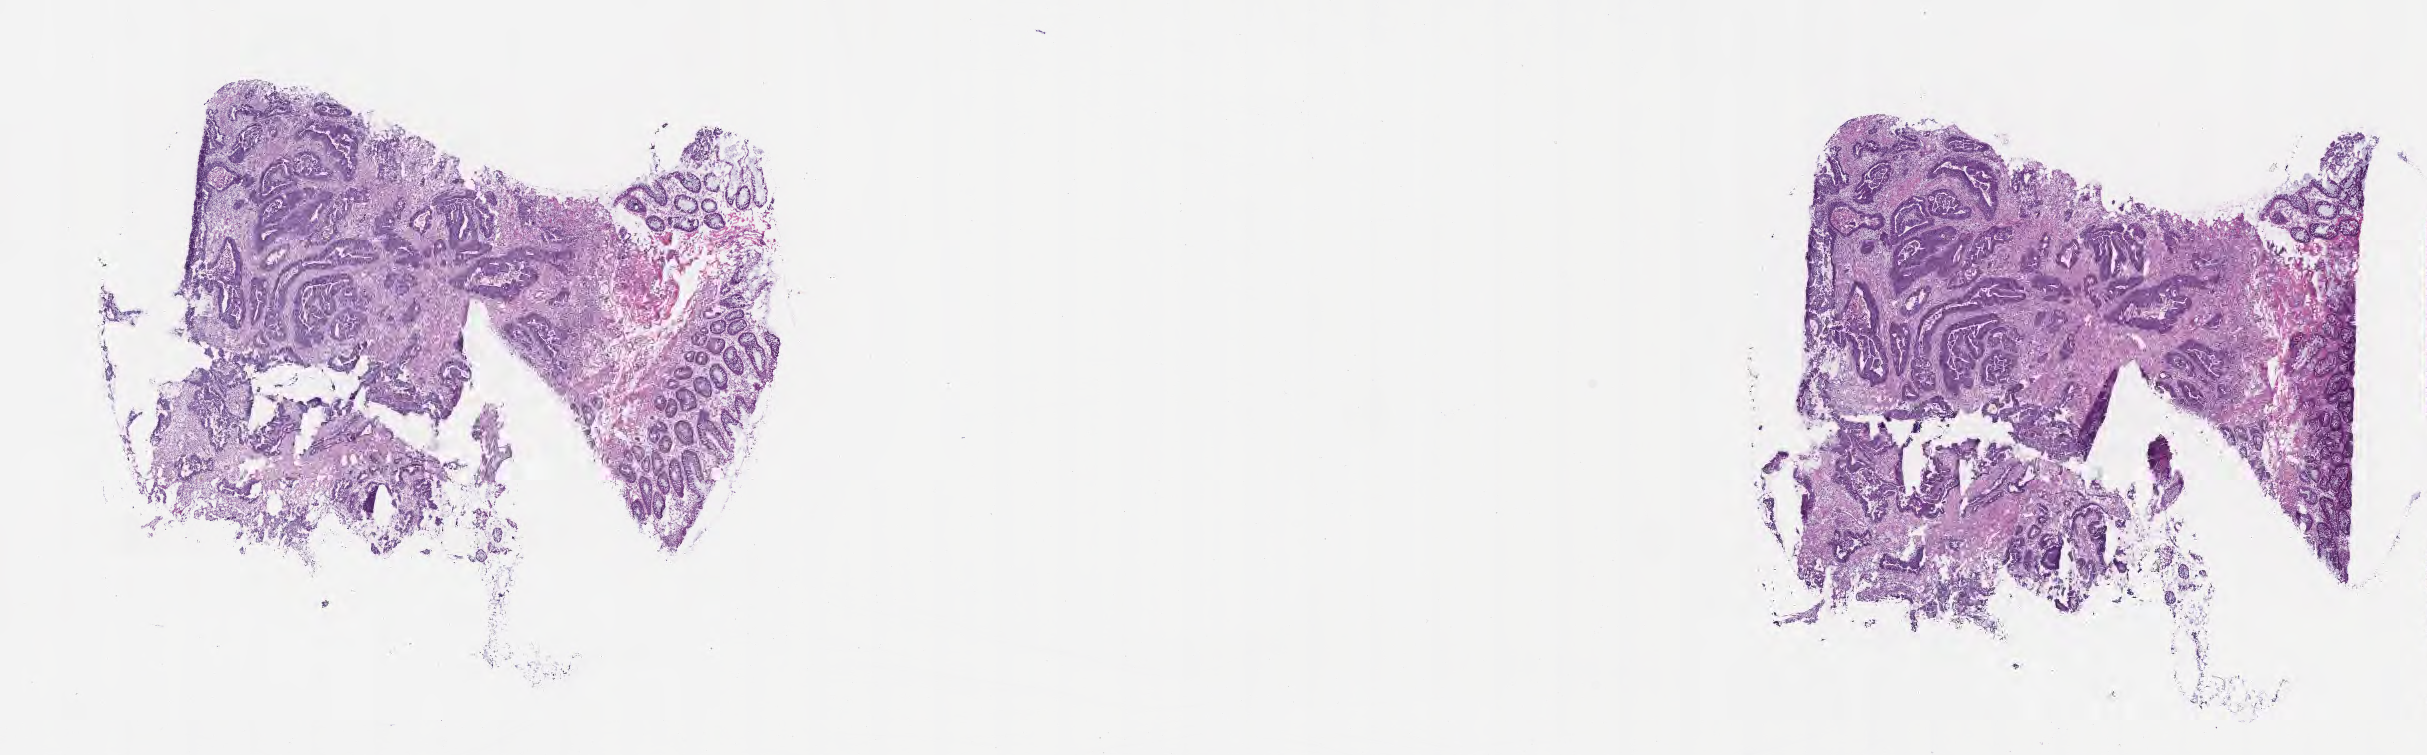
Whole-slide image, hematoxylin and eosin (H&E) stain — whole scanned area (about 19.6 x 6.1 mm) shown as a low-resolution overview; frozen section; specimen: primary tumor; site: sigmoid colon. Male patient; age at initial diagnosis 61 years. Tumor grade: GB (borderline). Pathologist review of this section (percent, as recorded): tumor cells 80%, tumor nuclei 80%, stromal cells 16%, necrosis 0%, normal cells 4%. Inflammatory infiltration, as recorded: lymphocyte infiltration 3%, monocyte infiltration 2%, neutrophil infiltration 7%.
Diagnosis: Adenocarcinoma, NOS. AJCC pathologic stage: Stage IIIB.